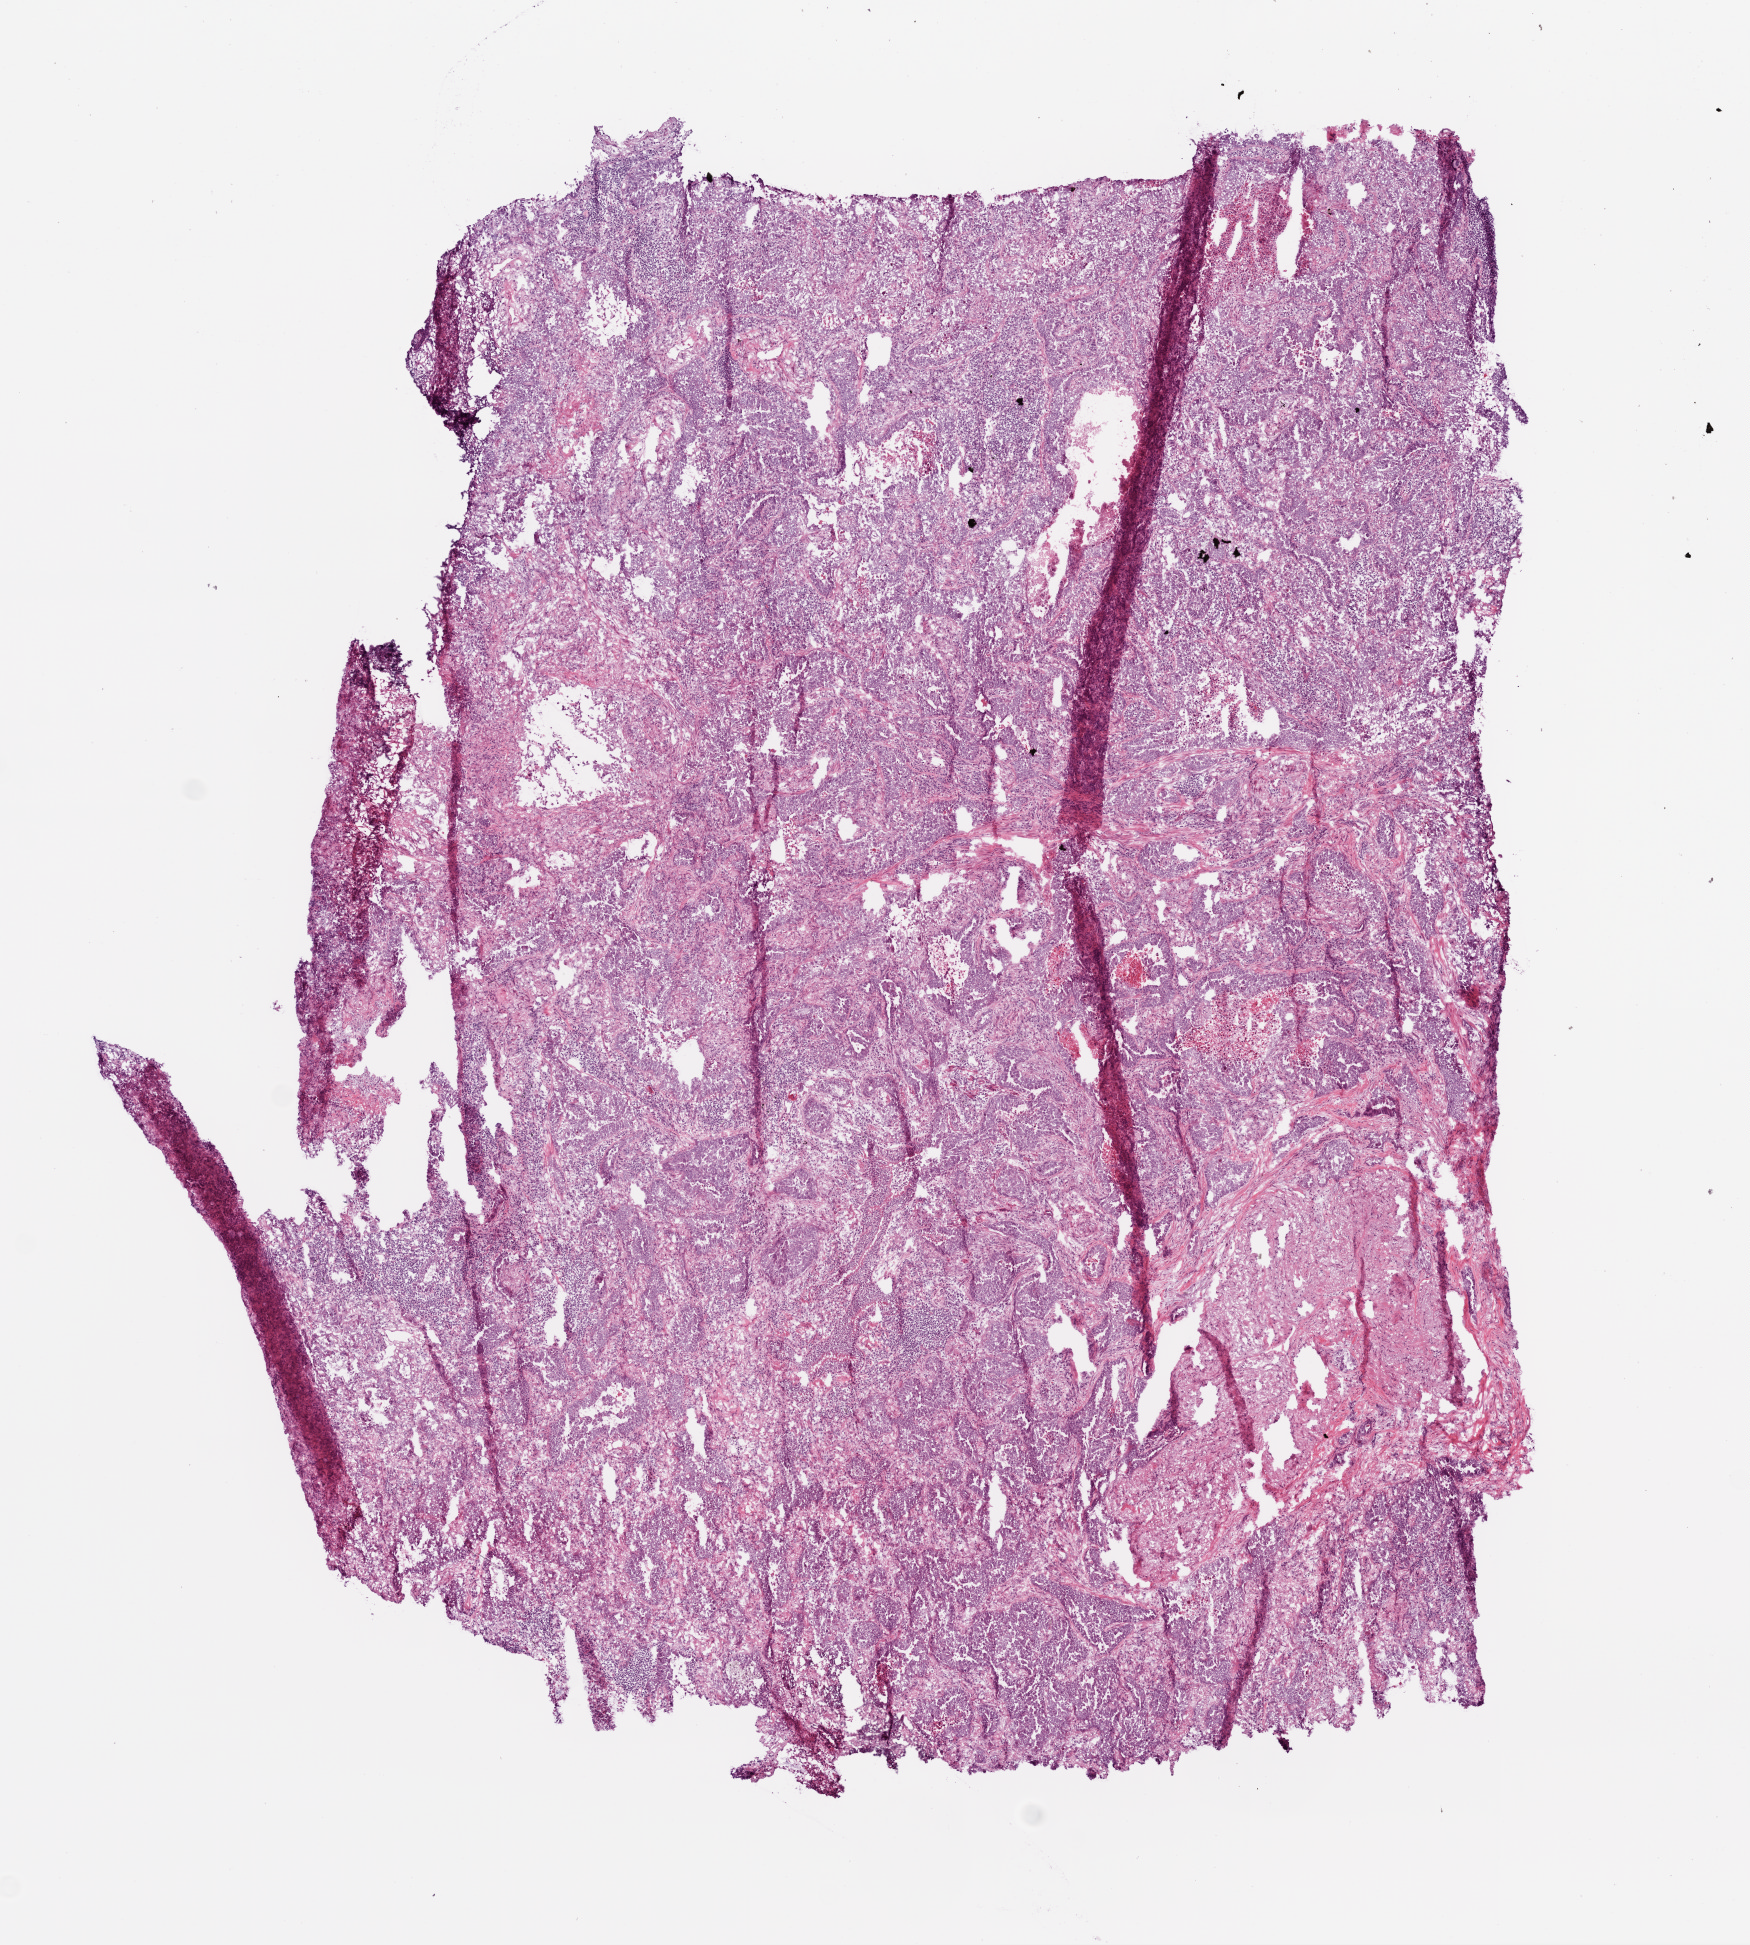
Digitized H&E-stained tissue section (whole slide), a low-resolution overview of the entire scanned area, about 7.0 x 7.8 mm, frozen section, lung, primary tumour sample. Female patient. Slide review estimates, as recorded: tumour cells 80%, tumour nuclei 65%, normal cells 0%, stromal cells 10%, necrosis 5%.
- diagnosis: Bronchiolo-alveolar carcinoma, non-mucinous (upper lobe, lung)
- AJCC pathologic stage: IB (6th edition)
- TNM: T2 N0 M0